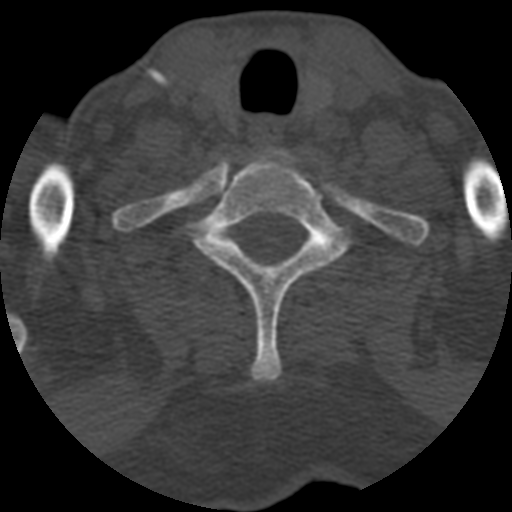
CT including the spine, one axial slice; position 518 of 708 along the scan axis; reconstruction kernel STANDARD; 120 kVp; one of 3 acquisitions stored at this slice position; bone window (W 1800 / L 400 HU); 512 × 512 image matrix, field of view 160 × 160 mm. Patient age 55 years. From the clinical record (not read from this slice): primary cancer: colon; vertebrae with lytic lesions (as recorded): T12, L1, L5.
Annotated regions visible in this slice (semi-automatically segmented with operator editing):
- T1 vertebra: bounding box [x1, y1, x2, y2] px = [186, 155, 348, 382]
- T2 vertebra: [226, 240, 237, 248]